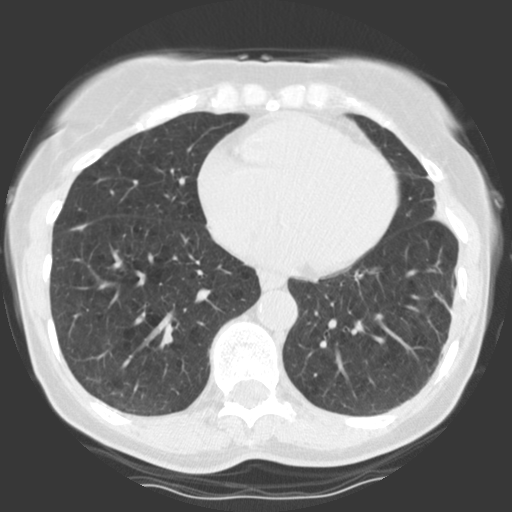
Chest CT (low-dose screening protocol), one axial image. First (baseline) screen. Lung window (W 1500 / L -600 HU). 2.5 mm slice thickness. Slice 44 of 123 in the series. 512 × 512 image matrix, field of view 290 × 290 mm. Female participant, aged 68 years at enrolment. Former smoker at enrolment.
Expert reader's lesion annotation, bounding box [x1, y1, x2, y2] px = [56, 211, 101, 253]. The screening reader recorded 2 non-calcified nodules or masses ≥4 mm on this exam; which of them this box marks is not recorded. Official screen result: positive, change unspecified: nodule(s) >= 4 mm or enlarging nodule(s), mass(es), or other non-specific abnormalities suspicious for lung cancer.